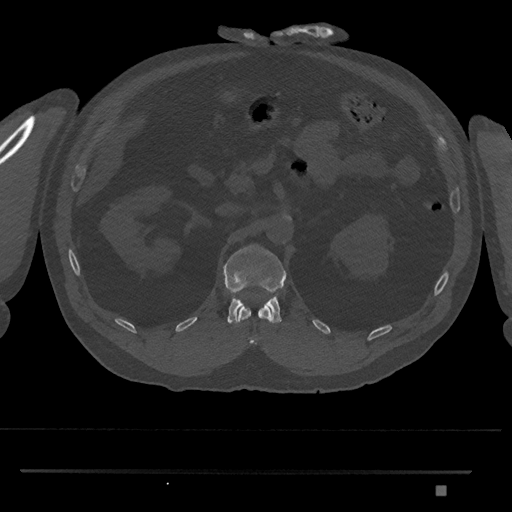
CT including the spine, one axial slice; position 850 of 1134 along the scan axis; reconstruction kernel Br40s/3; 120 kVp; bone window (W 1800 / L 400 HU); 0.5 mm slice thickness; 512 × 512 image matrix, field of view 429 × 429 mm. Patient: male, 65 years. Case-level facts recorded for this patient, not image findings: primary cancer: prostate.
Annotated regions visible in this slice (semi-automatic segmentation, software-assisted and operator-edited):
- L1 vertebra: bounding box (x1, y1, x2, y2) in pixels: (223, 244, 287, 324)
- T12 vertebra: (238, 305, 272, 344)